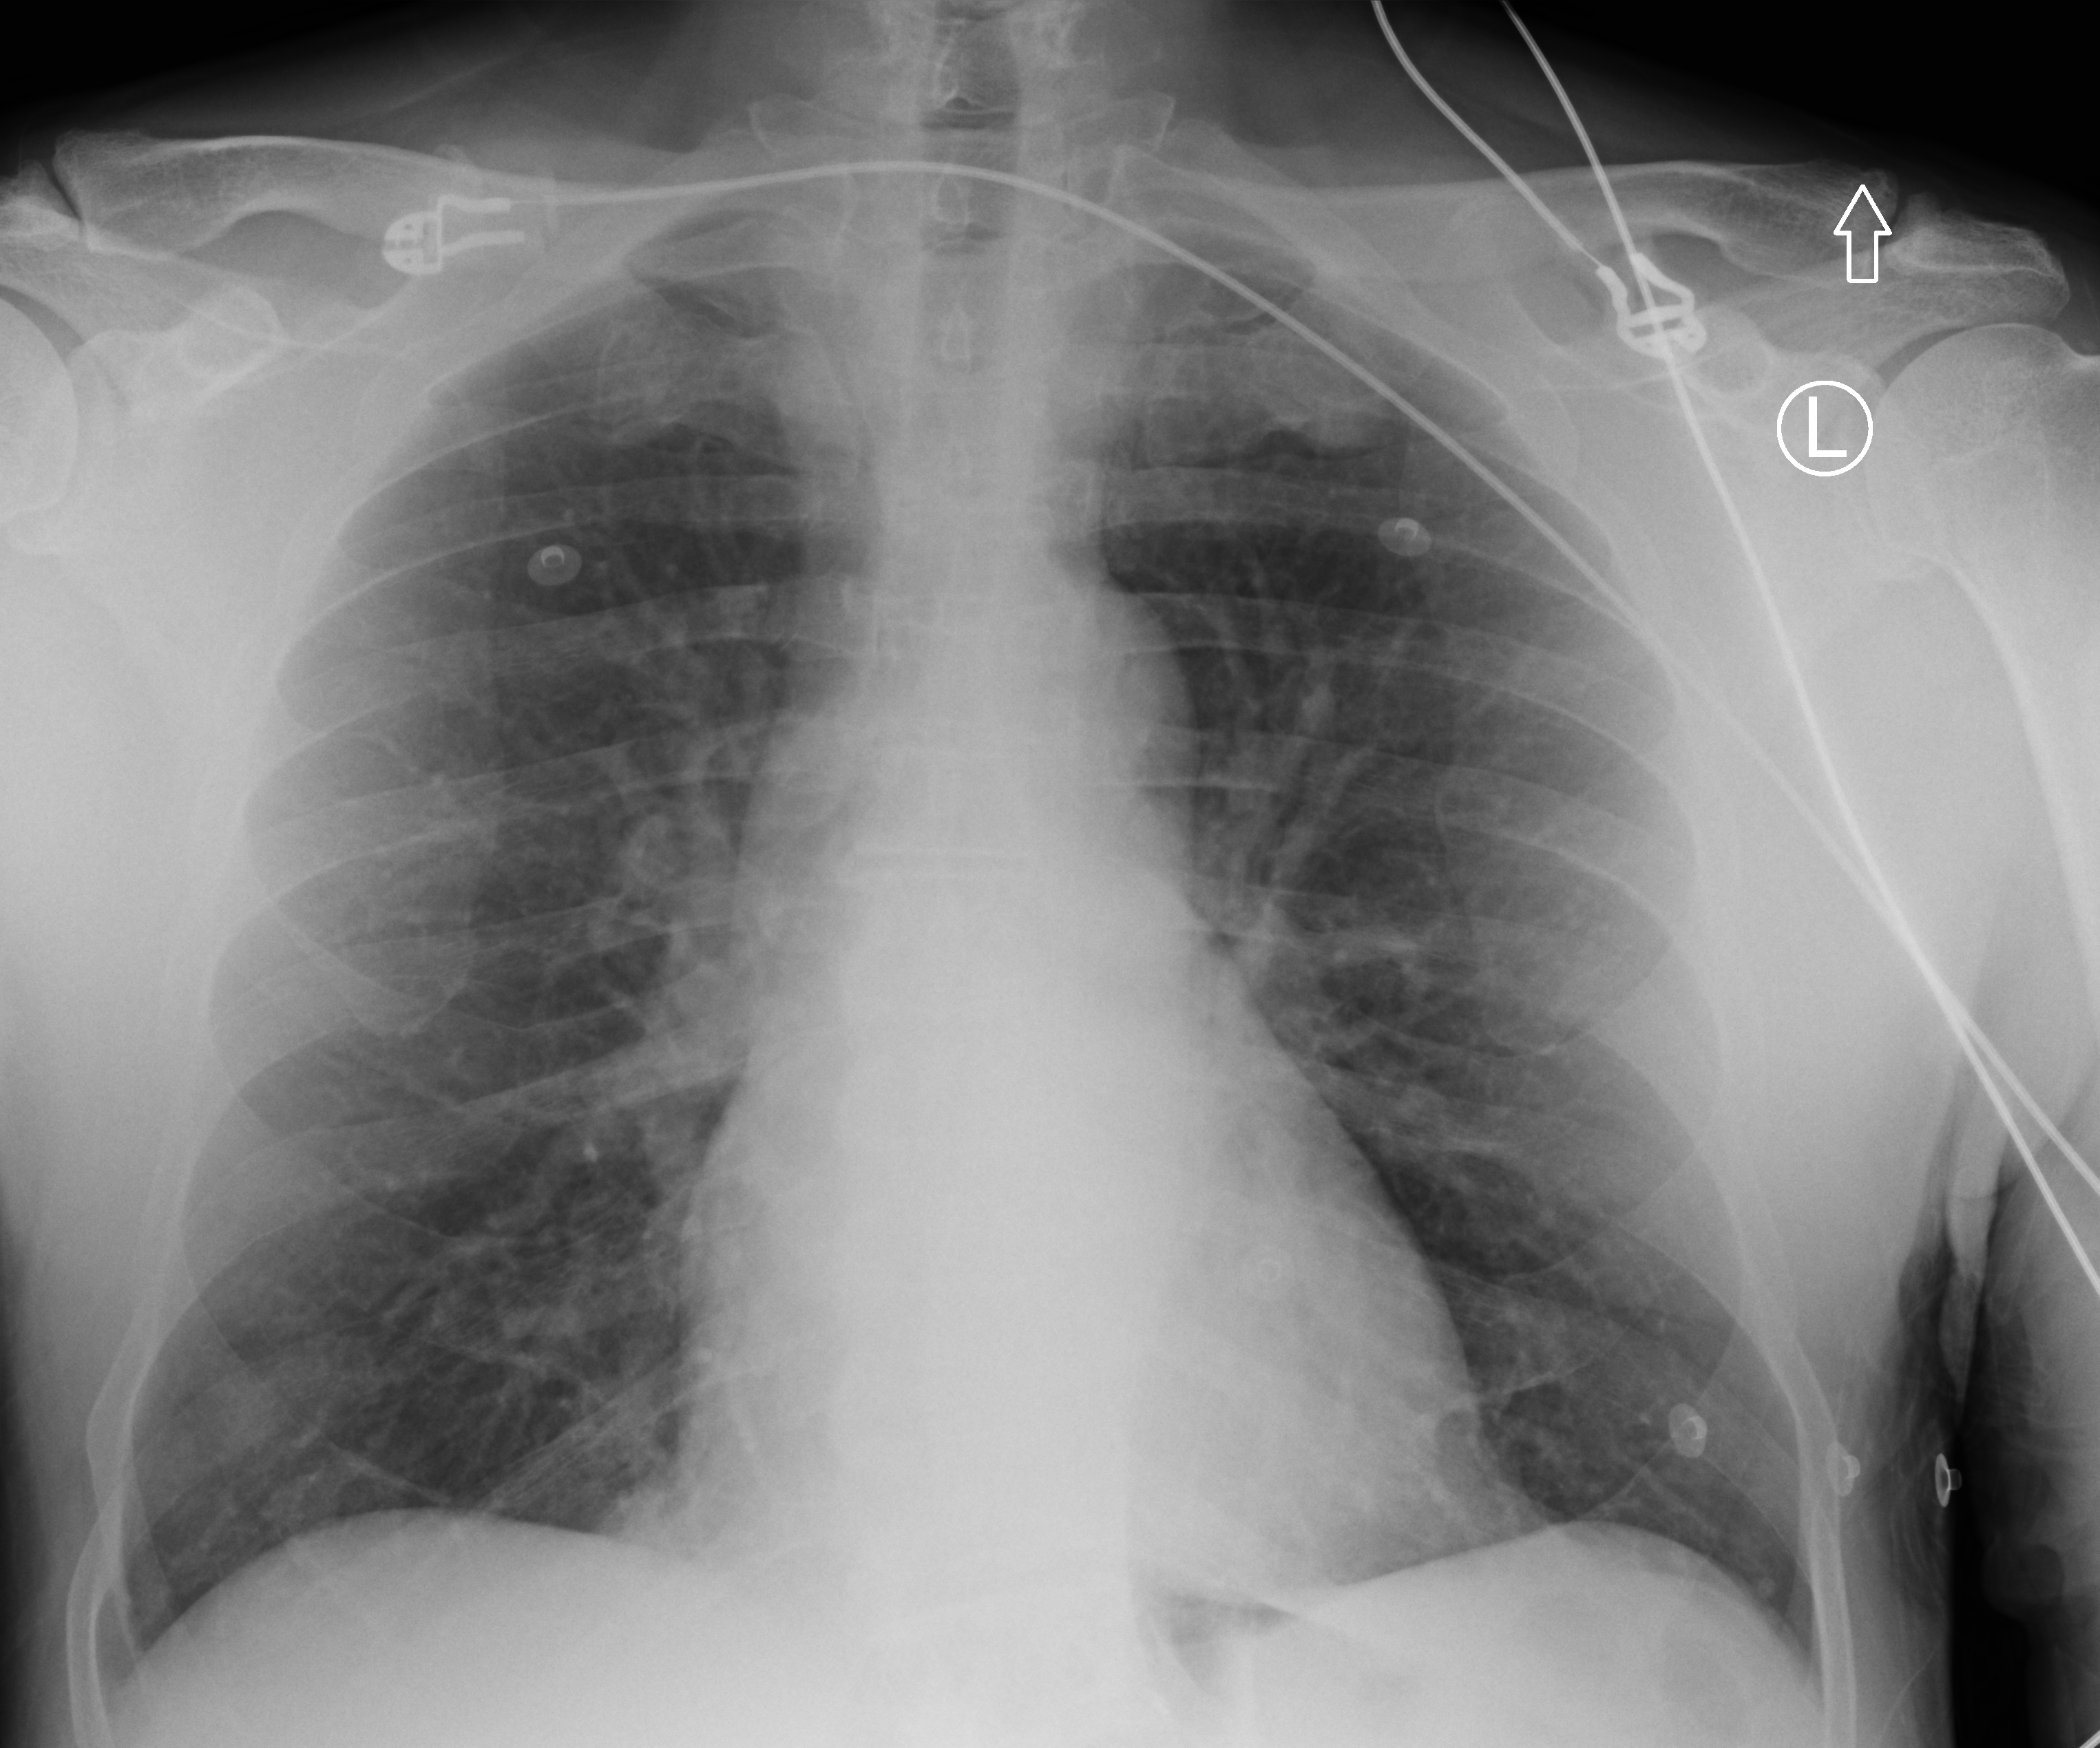
Chest X-ray (portable). Male patient hospitalised with COVID-19, age 18–59 years.
Hospital-stay facts (about this admission, not read from this image; timing relative to this image not recorded):
- admitted to intensive care during this hospital stay: no
- mechanically ventilated during this hospital stay: no
- diabetes (admission record): no